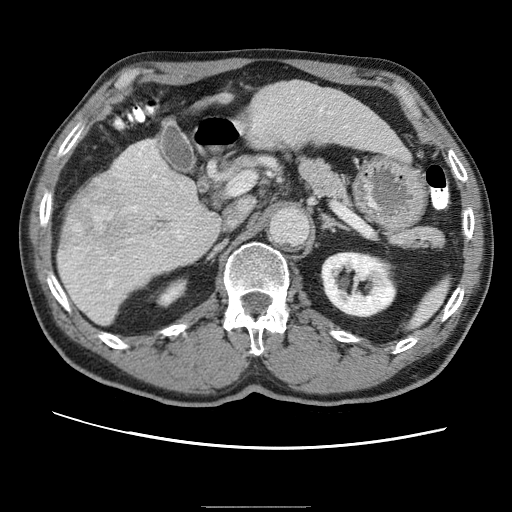
Contrast-enhanced abdominal CT (liver protocol), one axial slice. Position 25 of 75 along the scan axis. One of 2 acquisitions stored at this slice position. Soft-tissue window (W 400 / L 40 HU). 512 × 512 image matrix, field of view 360 × 360 mm. Case-level facts recorded for this patient, not image findings: diagnosis: hepatocellular carcinoma (patient treated with transarterial chemoembolisation; whether this scan precedes or follows treatment is not stated here); TNM stage (as recorded): Stage-II; Child-Pugh class: A; tumour differentiation: well differentiated; tumour nodularity: multinodular.
Annotated regions visible in this slice (semi-automatically segmented with operator editing):
- liver parenchyma outside the tumour (the mass and vessels are separate outlines, so this box may not span the whole liver): box from (x=58, y=84) to (x=383, y=324) px
- liver vessels: (x=69, y=96)–(x=262, y=284)